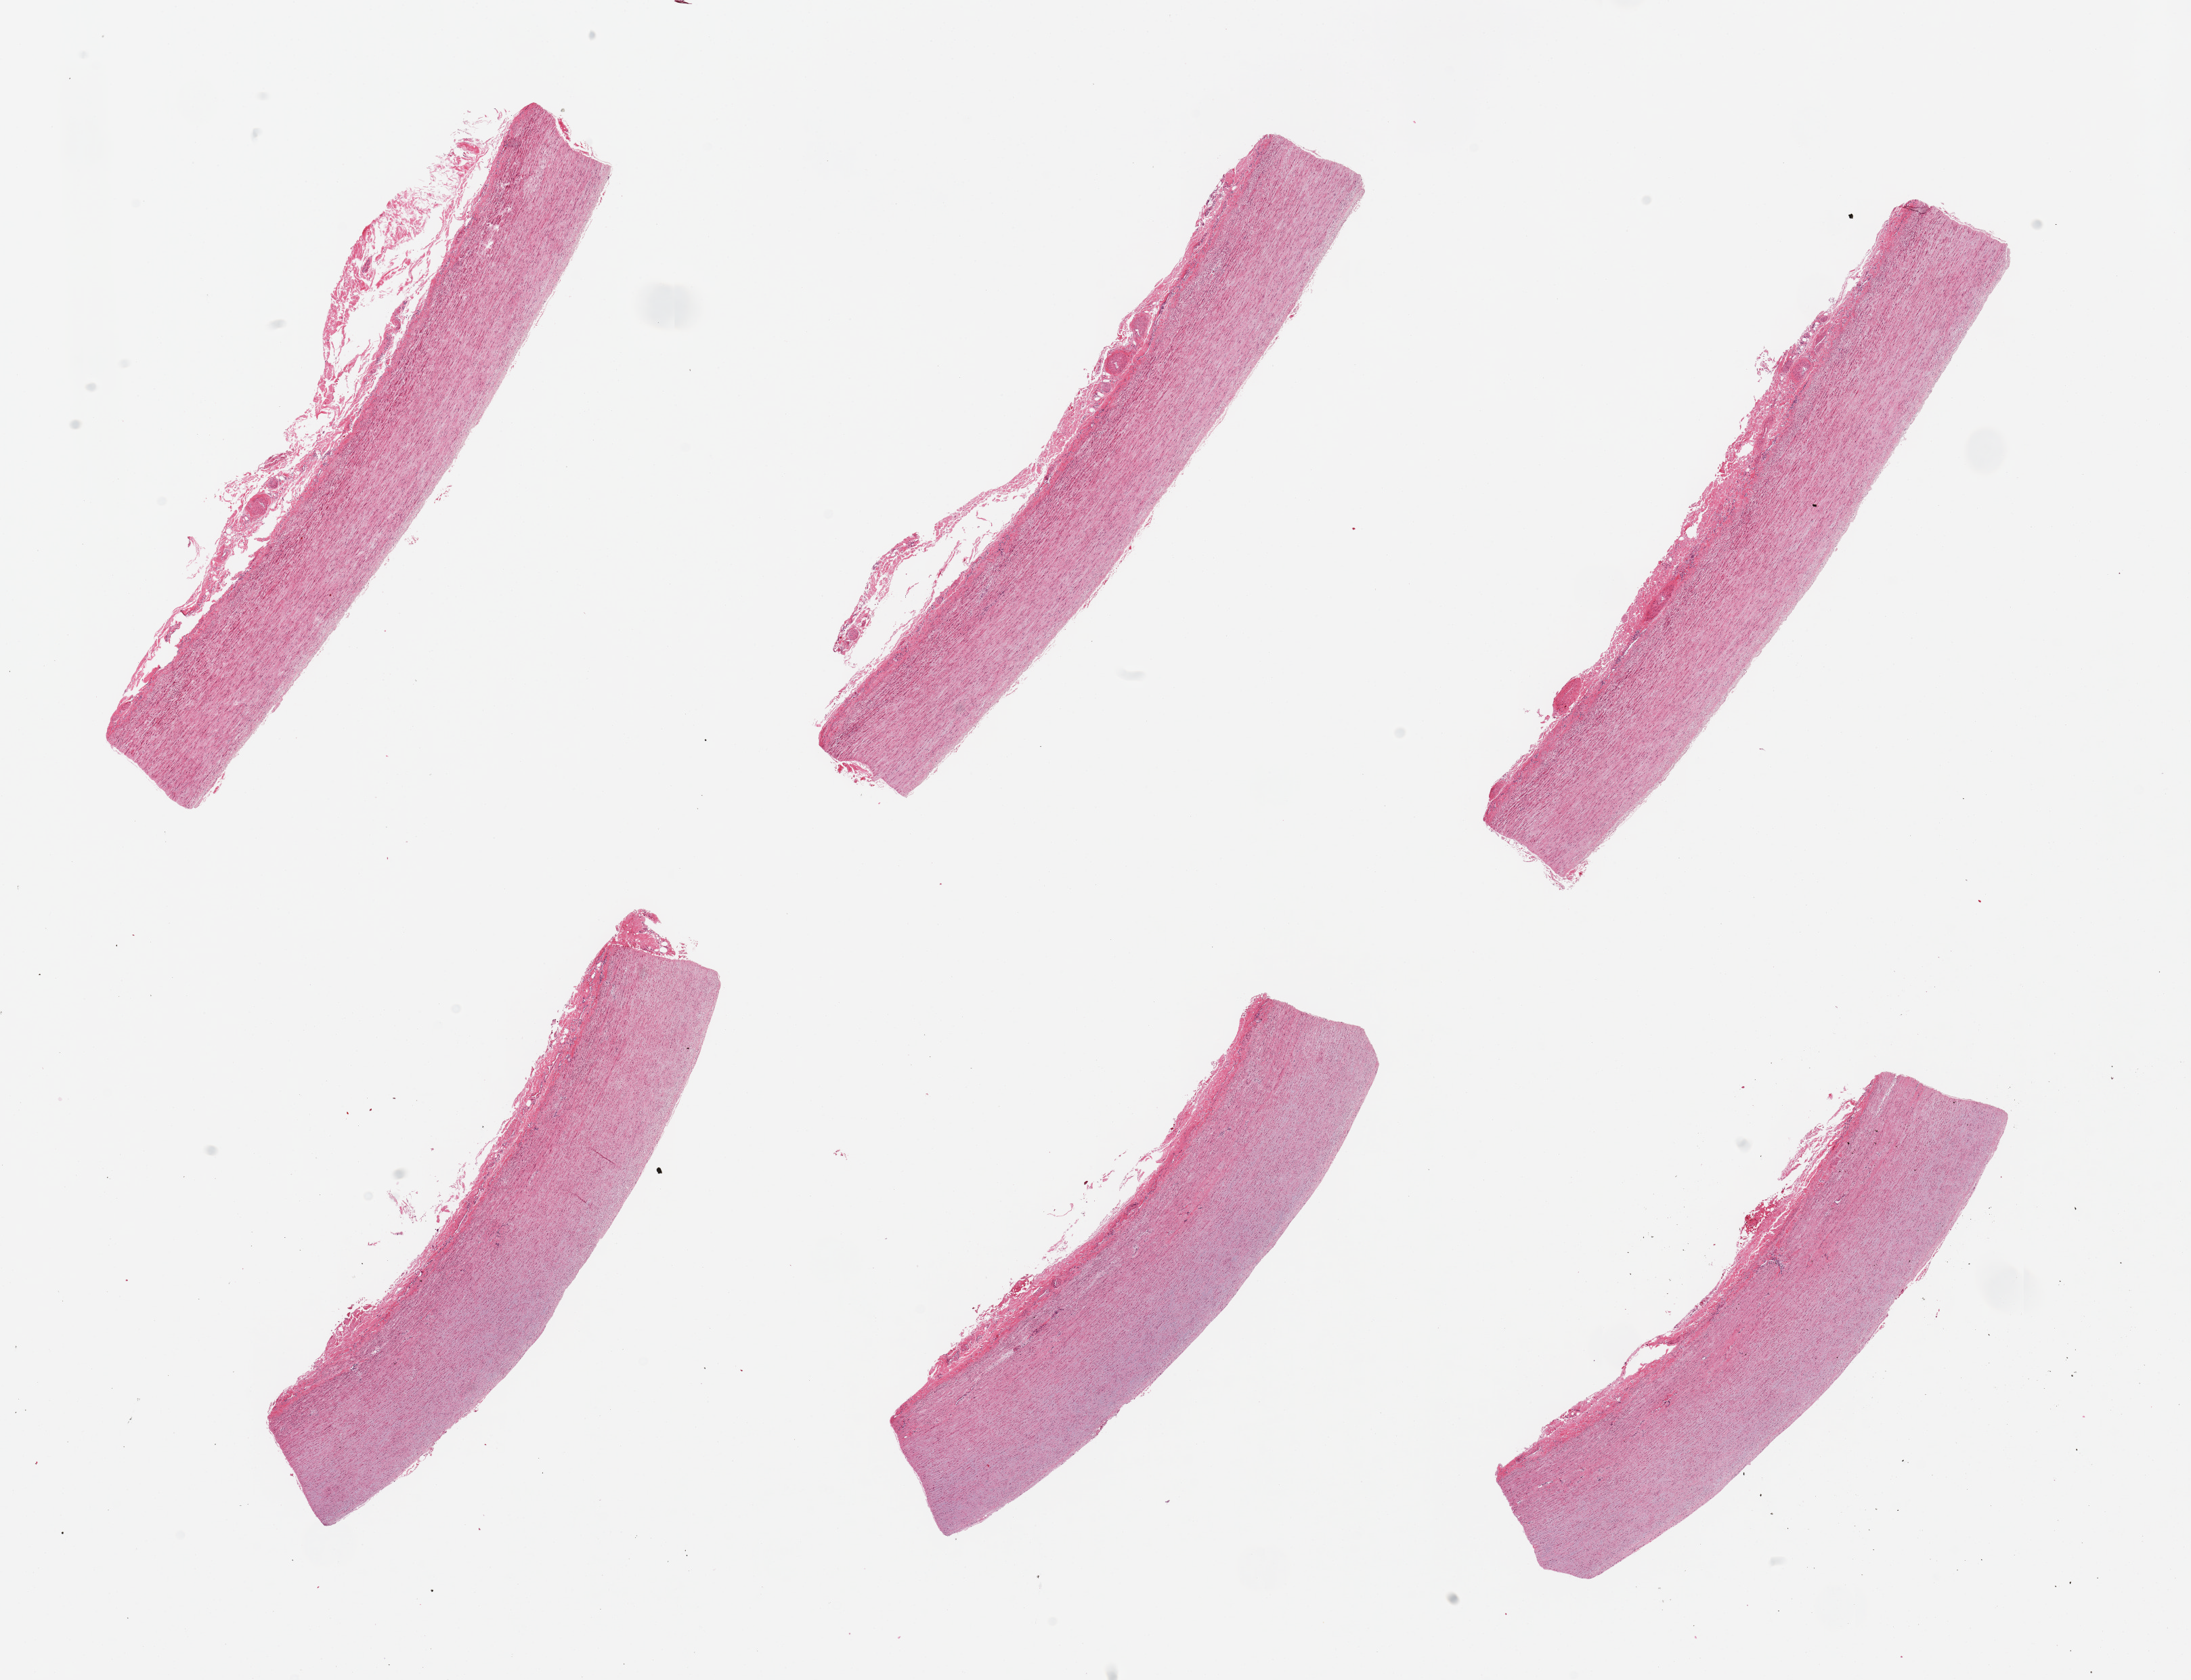
Haematoxylin and eosin whole-slide image — whole scanned area (about 25.6 x 19.6 mm, slide scanned at 20x) shown as a low-resolution overview; PAXgene-fixed, paraffin-embedded tissue; sampled site (target tissue): aorta; donor tissue sample. Donor: female.
Pathologist's review note for this sample: 6 pieces; well trimmed; no plaque.